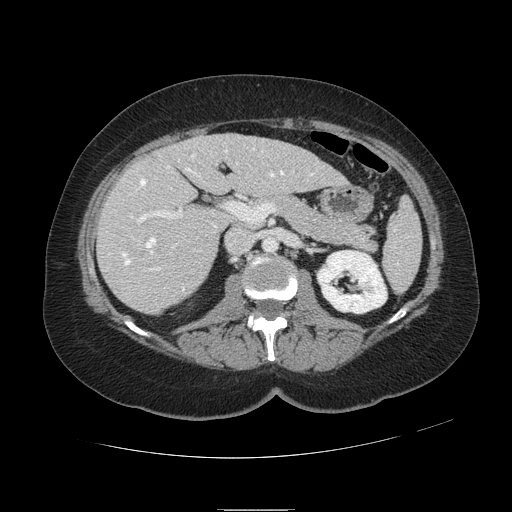
Contrast-enhanced abdominal CT, one axial slice; position 49 of 121 along the scan axis; 120 kVp; intravenous contrast given; soft-tissue window (W 400 / L 40 HU); 2.5 mm slice thickness; 512 × 512 image matrix, field of view 400 × 400 mm. Female patient, age 52 years. Case-level facts recorded for this patient, not image findings: diagnosis: colorectal cancer liver metastases, imaged before liver resection; multiple liver metastases: yes; largest metastasis: 6.3 cm; disease in both lobes: no.
Annotated regions visible in this slice (expert manual segmentation):
- hepatic veins: box from (x=123, y=149) to (x=313, y=291) px
- liver: (x=99, y=134)–(x=345, y=313)
- planned liver remnant (the part of the liver to remain after resection): (x=173, y=134)–(x=345, y=196)
- portal vein (with intrahepatic branches): (x=130, y=163)–(x=293, y=270)